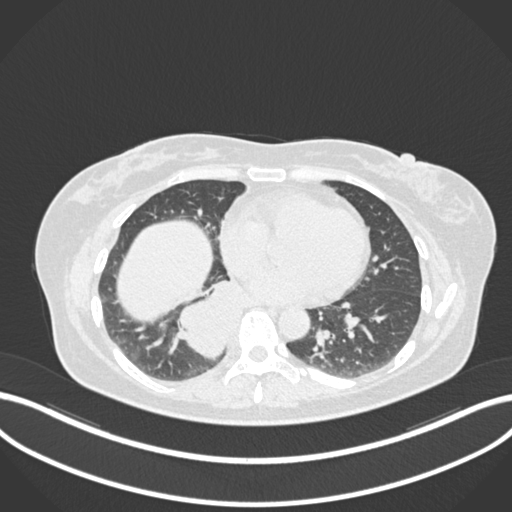
Chest CT, one axial slice; position 560 of 677 along the scan axis; lung window (W 1500 / L -600 HU); 512 × 512 image matrix. Female patient, age 54 years. Case-level facts recorded for this patient, not image findings: clinical TNM (as recorded): T4 N0 M0.
Structures marked on this image (bounding box drawn by a radiologist):
- lung tumour (recorded histology: adenocarcinoma): bounding box (x1, y1, x2, y2) in pixels: (175, 275, 258, 363)